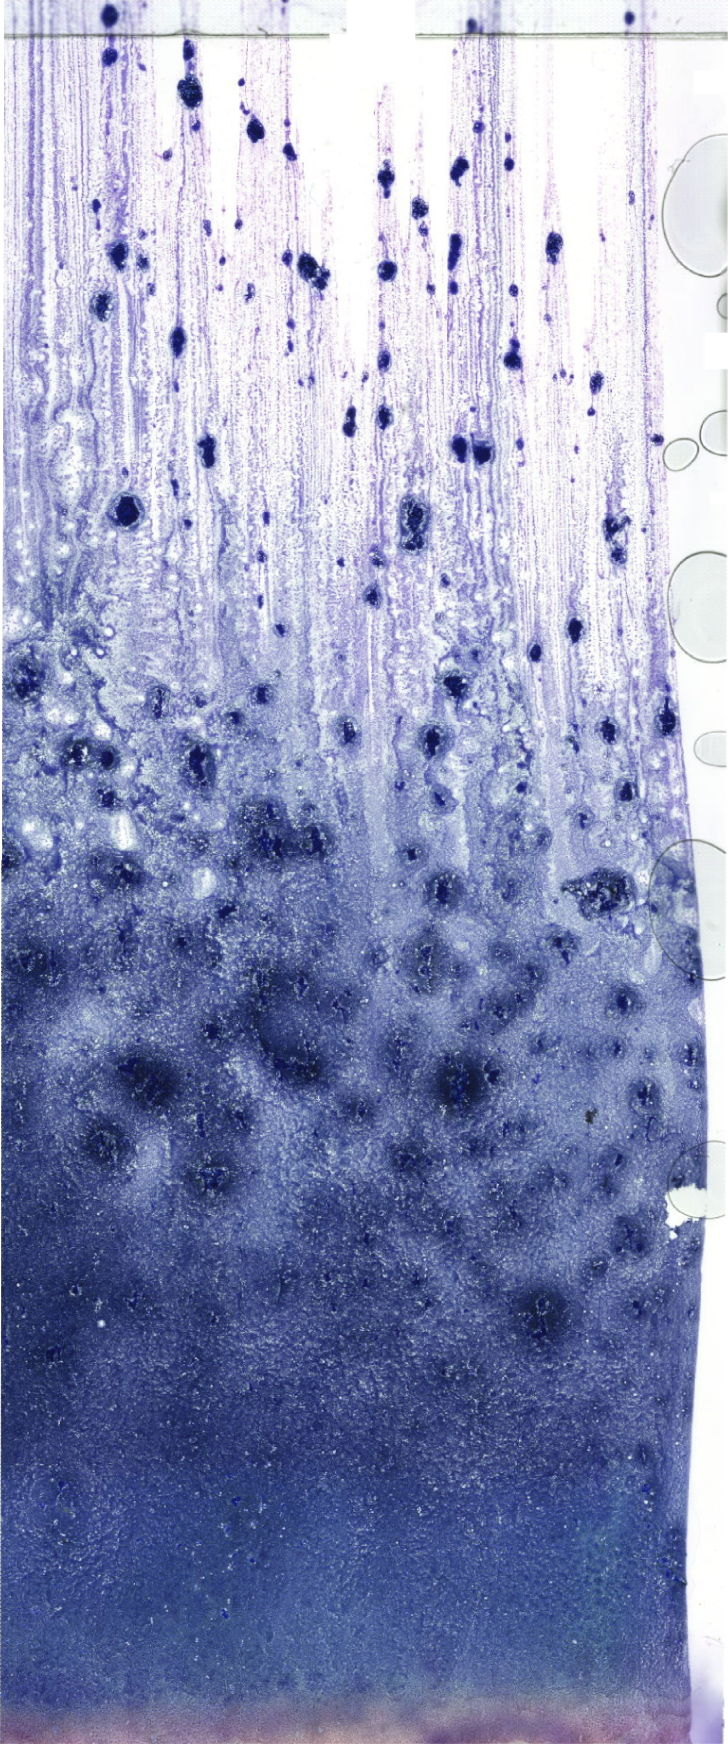
Bone marrow aspirate smear, May-Grünwald-Giemsa (MGG) stain, whole-slide image — a low-resolution overview of the entire scanned area, about 20.6 x 49.4 mm. Female patient.
Diagnosis: Mixed Phenotype Acute Leukemia, B/Myeloid.